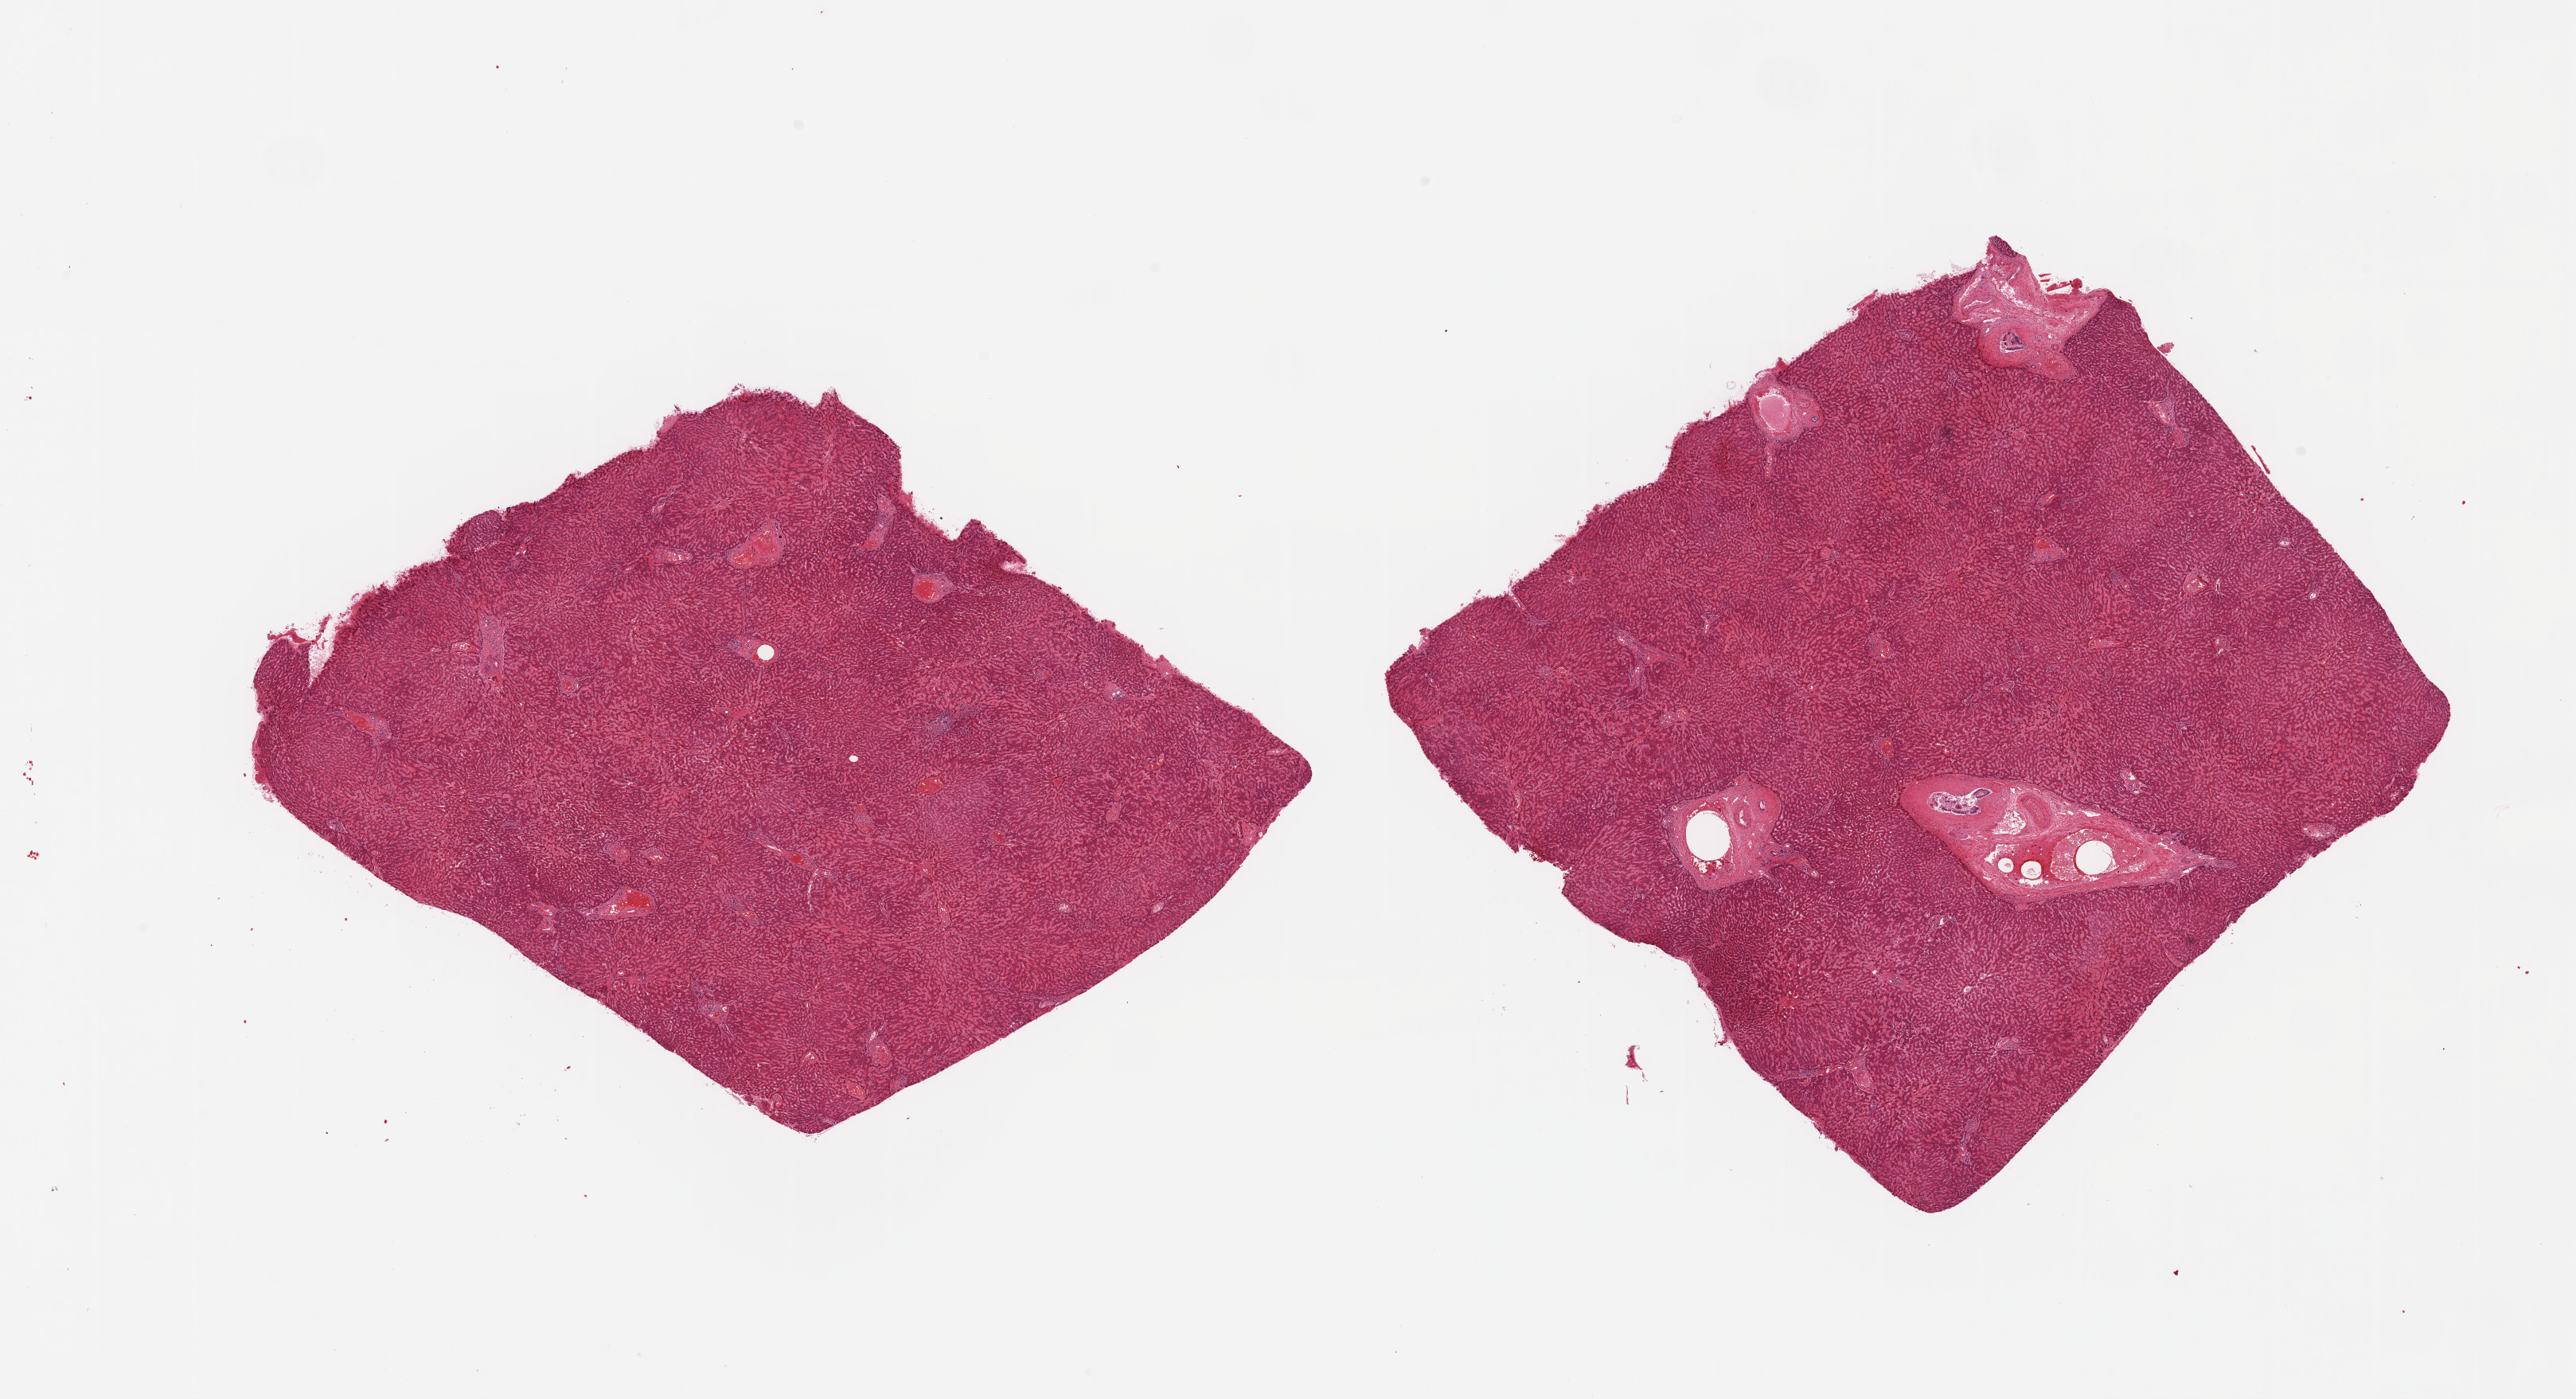
Haematoxylin and eosin whole-slide image — shown as a low-resolution overview of the whole scanned area (about 25.6 x 13.9 mm). PAXgene-fixed, paraffin-embedded tissue. Sampled site (target tissue): liver. Tissue donor sample.
Review note (as recorded): 2 pieces, mild passive congestion.